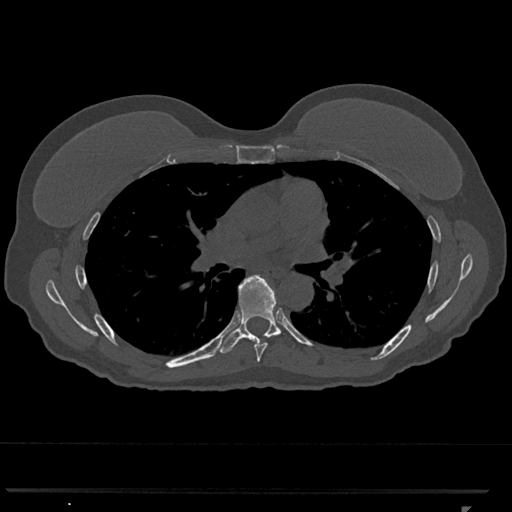
CT including the spine, one axial slice. Reconstruction kernel Br40s/3. 120 kVp. Bone window (W 1800 / L 400 HU). 0.5 mm slice thickness. 512 × 512 image matrix, field of view 380 × 380 mm. Female patient, age 62 years. Case-level facts recorded for this patient, not image findings: primary cancer: renal.
Annotated regions visible in this slice (semi-automatic segmentation, software-assisted and operator-edited):
- T6 vertebra: bounding box [x1, y1, x2, y2] px = [254, 285, 271, 362]
- T7 vertebra: [217, 275, 294, 354]